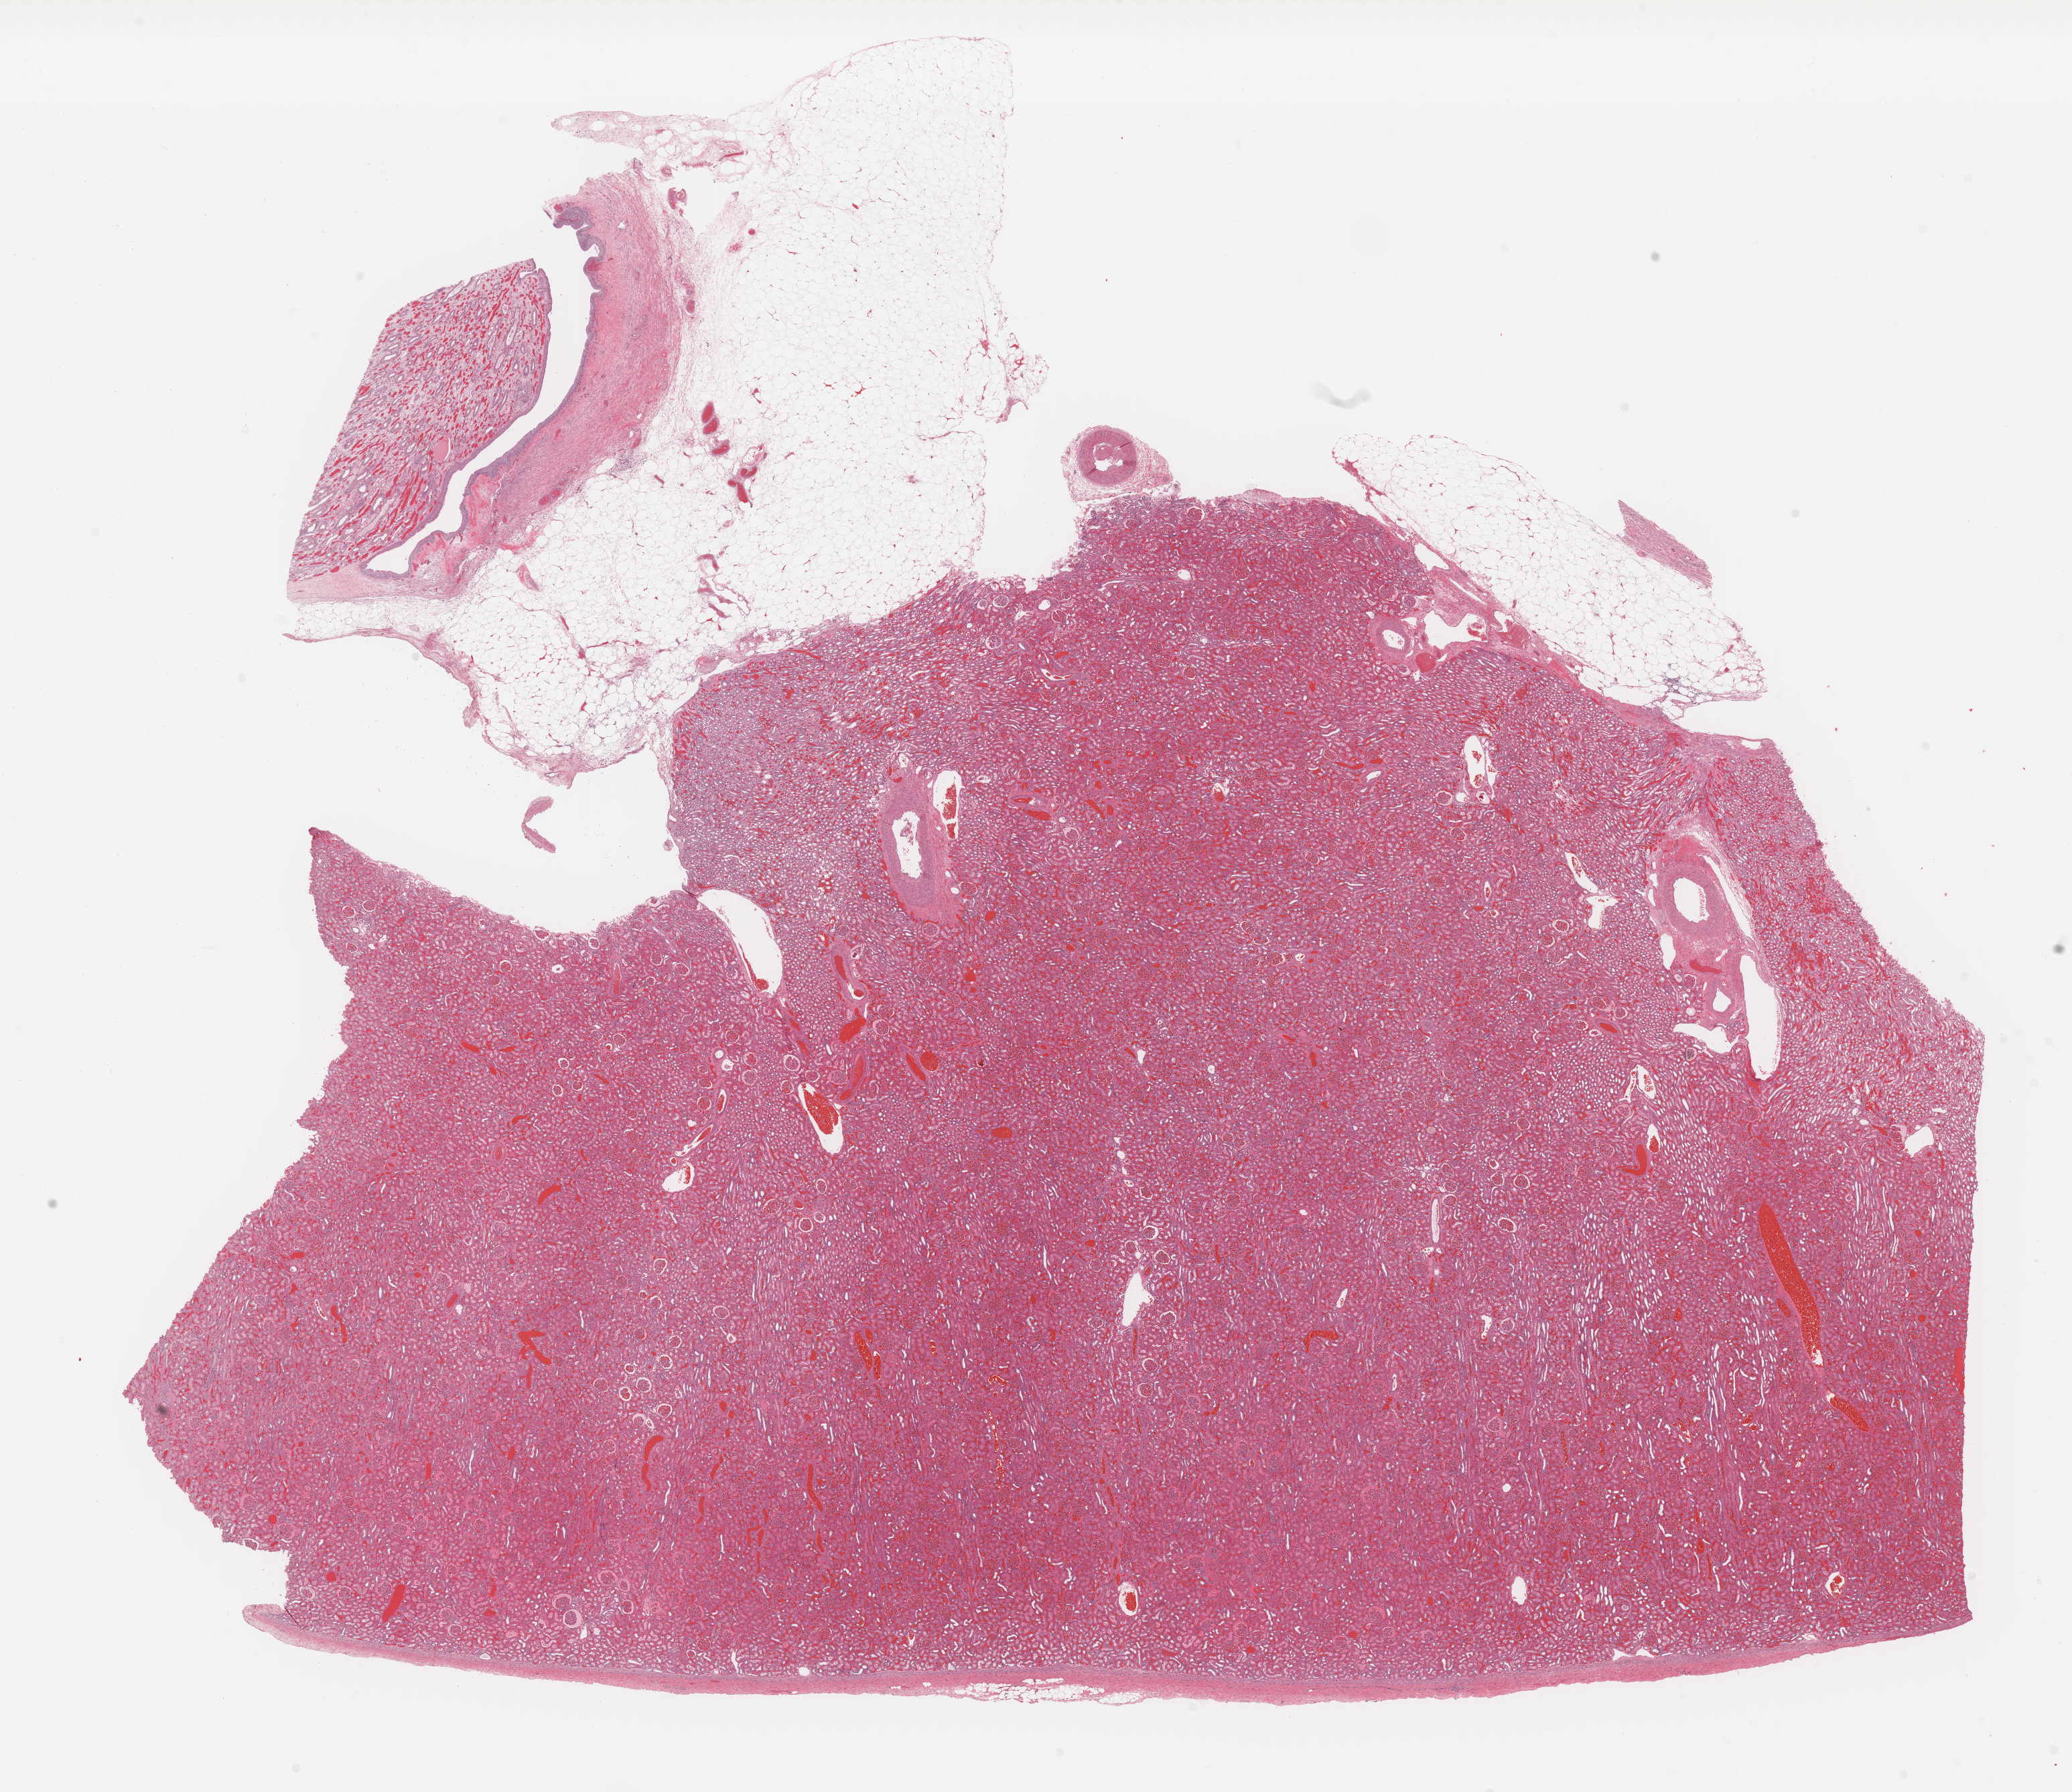
H&E whole-slide image — shown as a low-resolution overview of the whole scanned area (about 24.5 x 21.2 mm), formalin-fixed paraffin-embedded (FFPE) diagnostic section, solid tissue normal (non-tumour tissue) sample from the kidney. Male patient; age at initial diagnosis 40 years. Pathologist review of this section (percent, as recorded): tumour cells 0%, tumour nuclei 0%, normal cells 60%, stromal cells 40%, necrosis 0%. Inflammatory infiltration, as recorded: lymphocyte infiltration 0%, monocyte infiltration 0%, neutrophil infiltration 0%.
- this section: solid tissue normal (non-tumour) sample from the same patient
- patient diagnosis: Renal cell carcinoma, chromophobe type